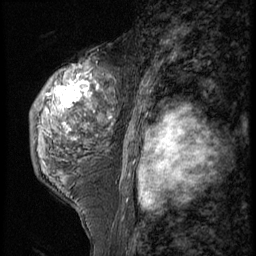
Breast MRI (dynamic contrast-enhanced), one sagittal slice; position 36 of 56 along the scan axis; 3 images stored at this slice position (order not interpretable as contrast timing); 1.5 T; TE 4.2 ms, TR 9 ms; 256 × 256 image matrix. Female patient, age 50 years. Case-level facts recorded for this patient, not image findings: setting: breast cancer imaged before/during neoadjuvant chemotherapy; receptor status: triple-negative.
Outlined on this slice (semi-automatically segmented with operator editing):
- analysis volume of interest (the breast-tissue region the enhancement analysis was run in; not a lesion): bounding box <29,50,122,191> (left, top, right, bottom; pixels)
- tumour enhancement mask (voxels above the 140 % enhancement threshold inside the analysis volume of interest): <61,81,90,109>